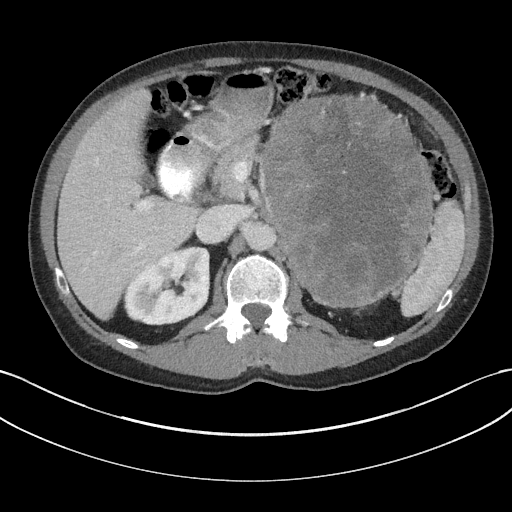
Contrast-enhanced abdominal CT, one axial slice. Position 109 of 147 along the scan axis. Reconstruction kernel I31f/3. 100 kVp. Intravenous contrast given. Soft-tissue window (W 400 / L 40 HU). 3 mm slice thickness. 512 × 512 image matrix, field of view 384 × 384 mm. Male patient, age 58 years. From the clinical record (not read from this slice): diagnosis: adrenocortical carcinoma; tumour side: left adrenal; tumour size at pathology: 22 cm; Ki-67 index: 26 %.
Outlined on this slice (semi-automatic segmentation, software-assisted and operator-edited):
- mass: box from (x=265, y=98) to (x=432, y=306) px